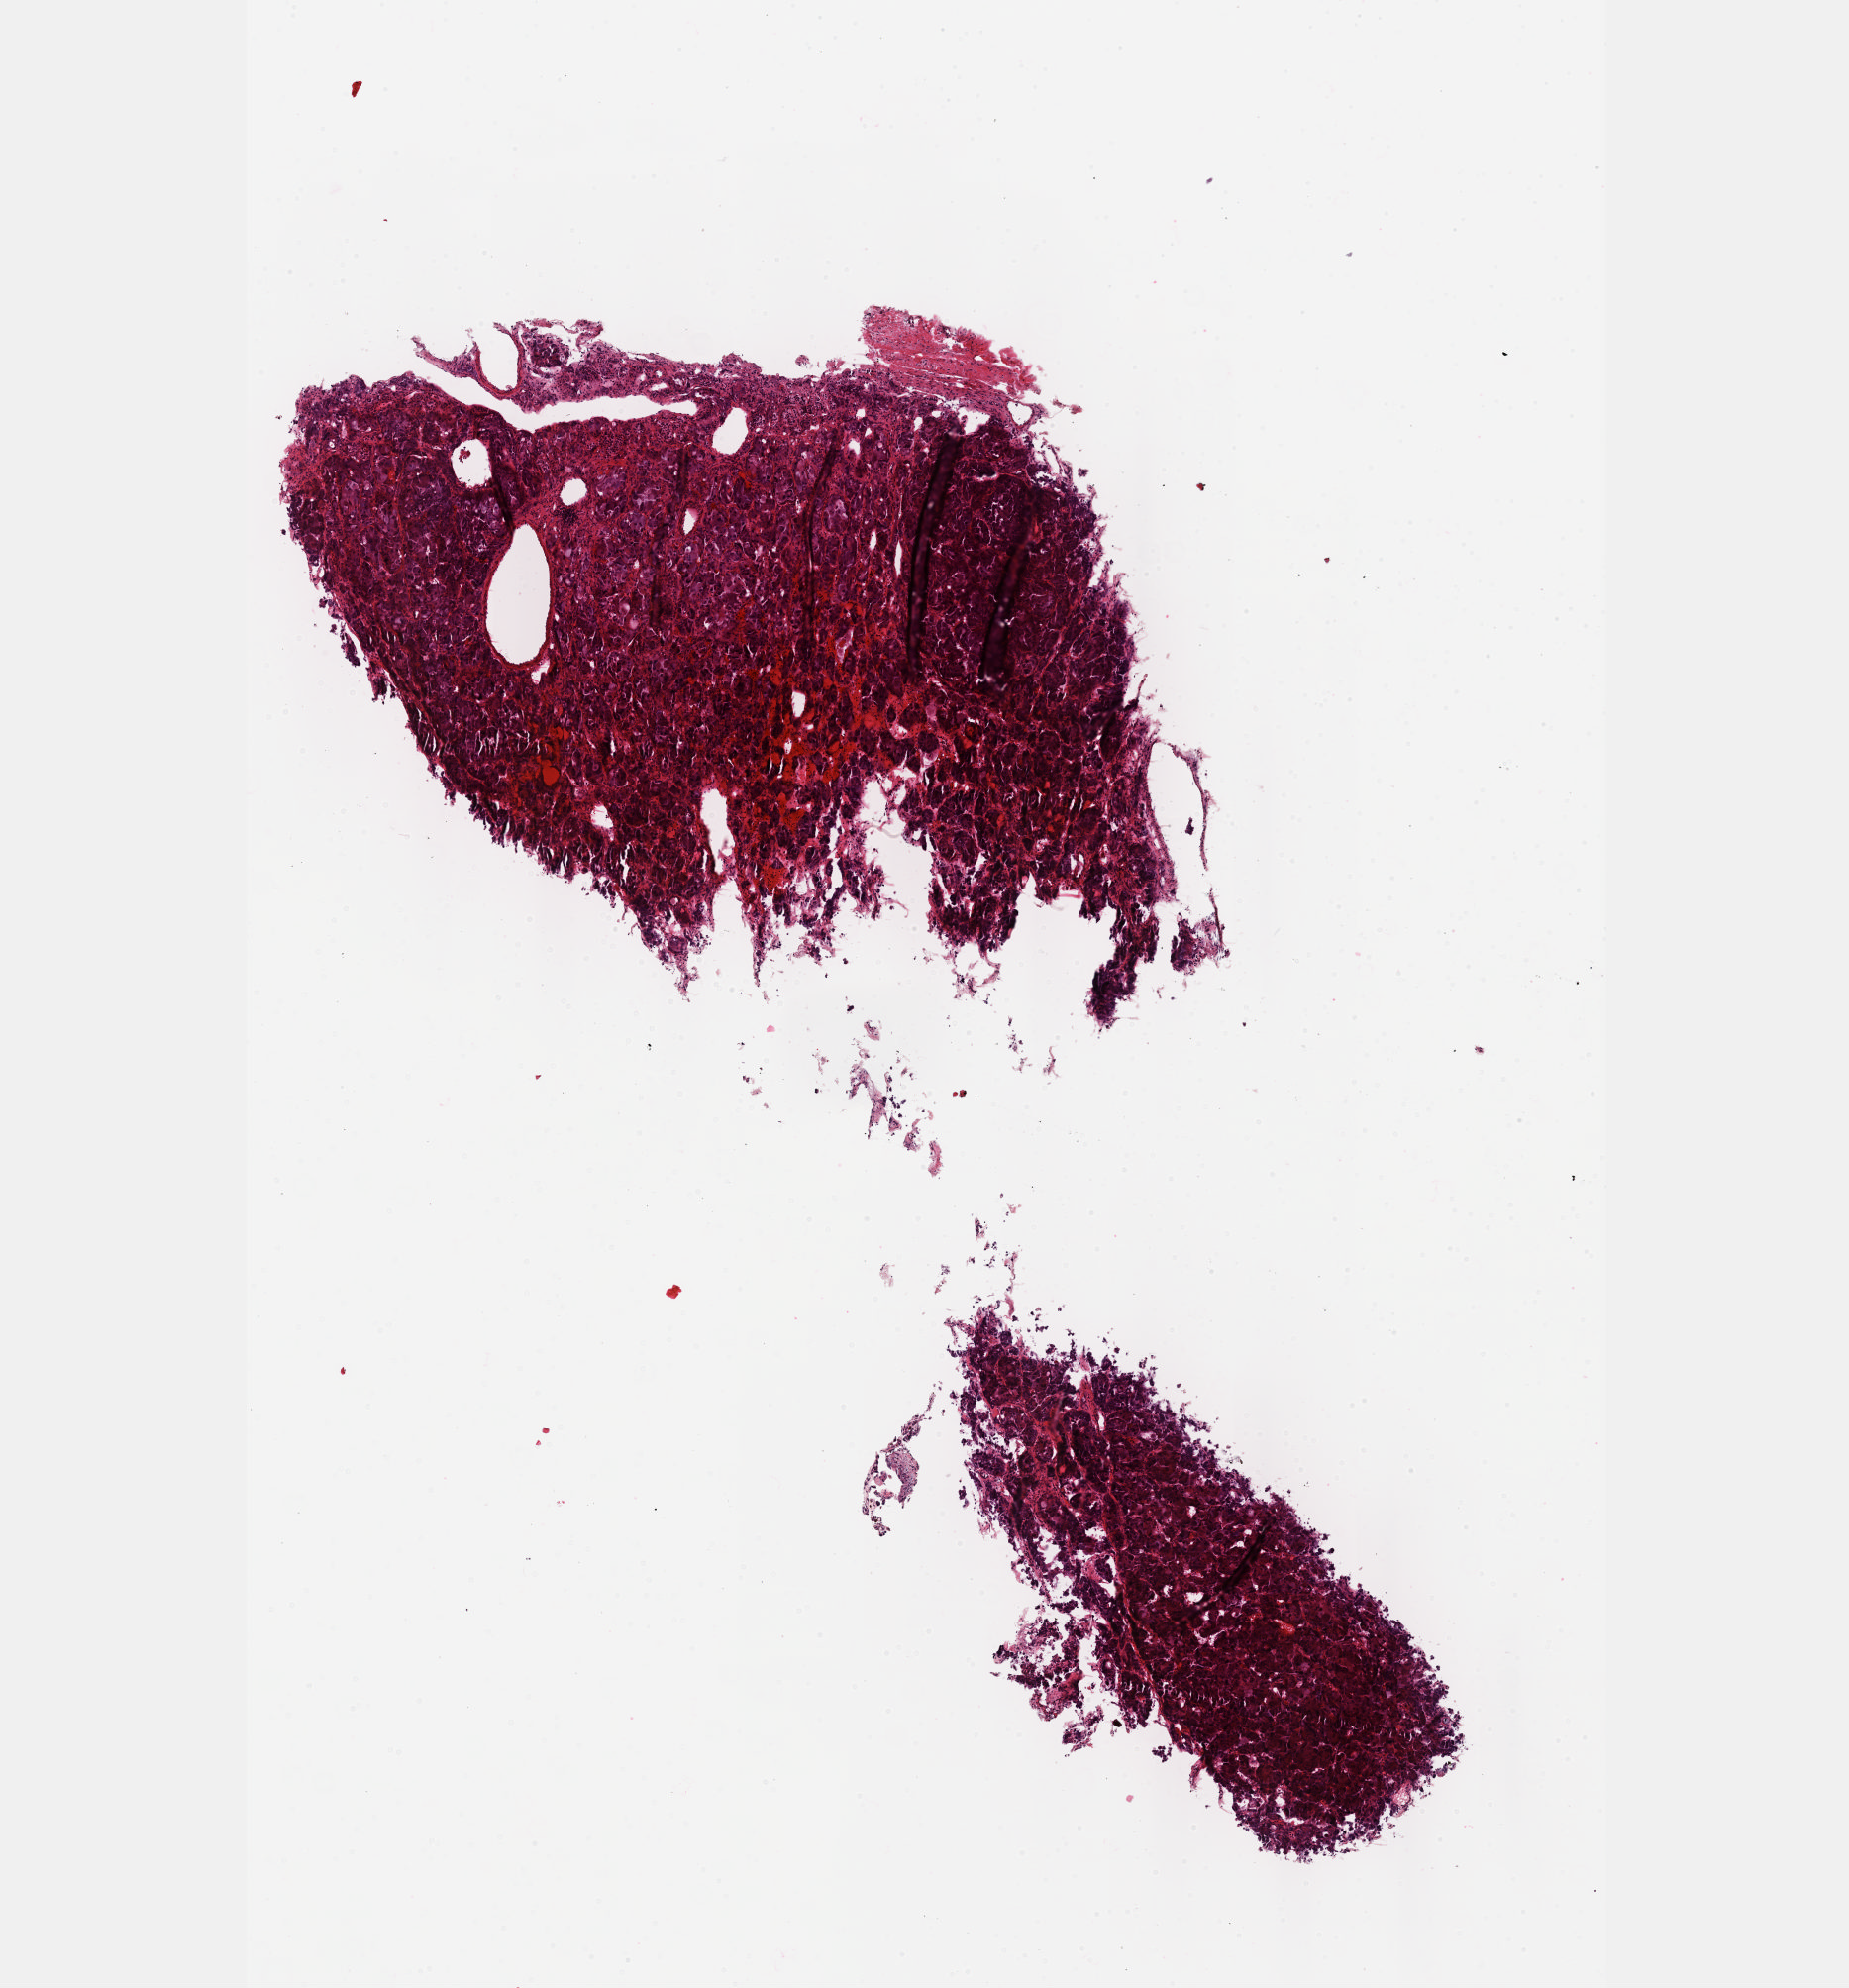
H&E-stained whole-slide image — shown as a low-resolution overview of the whole scanned area (about 7.5 x 8.1 mm); FFPE section; primary tumour sample from the adrenal gland. Patient: male, age at initial diagnosis 45 years.
Histologic diagnosis: Pheochromocytoma, NOS.